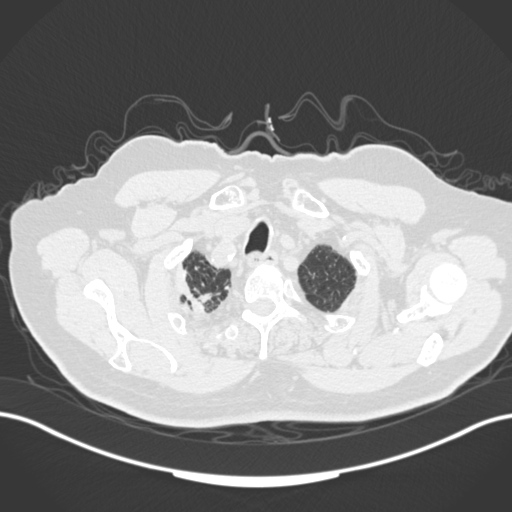
Chest CT, one axial slice. Slice 159 of 205 in the series (ordered by position). Reconstruction kernel B30f. 120 kVp. Lung window (W 1500 / L -600 HU). 1 mm slice thickness. 512 × 512 image matrix. Male patient, age 72 years. Case-level facts recorded for this patient, not image findings: clinical TNM (as recorded): T1a N0 M0.
Outlined on this slice (bounding box drawn by a radiologist):
- lung tumour (recorded histology: squamous cell carcinoma): box from (x=176, y=271) to (x=208, y=318) px